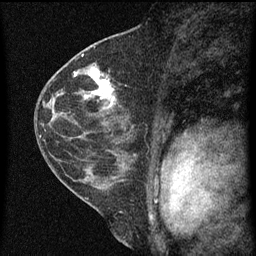
Breast MRI (dynamic contrast-enhanced), one sagittal slice. Position 34 of 60 along the scan axis. Dynamic contrast-enhanced series, image 2 of 3 at this slice position (ordered by acquisition). 1.5 T. TE 4.2 ms, TR 8 ms. 2 mm slice thickness. 256 × 256 image matrix, field of view 180 × 180 mm. Patient: female, 48 years.
Outlined on this slice (semi-automatic segmentation, software-assisted and operator-edited):
- analysis volume of interest (the breast-tissue region the enhancement analysis was run in; not a lesion): box from (x=82, y=68) to (x=126, y=125) px
- tumour enhancement mask (voxels above the 70 % enhancement threshold inside the analysis volume of interest): (x=85, y=68)–(x=116, y=107)